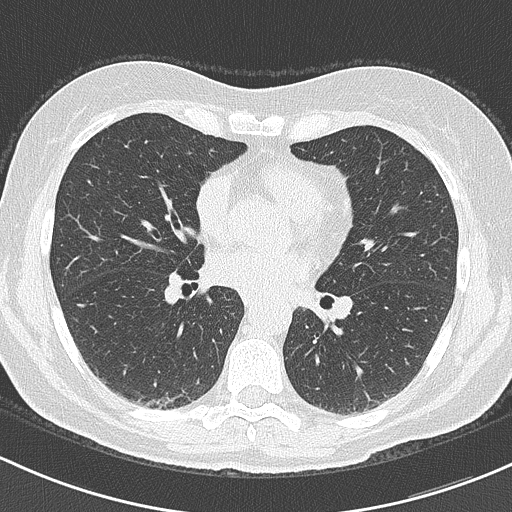
Low-dose screening chest CT, one axial slice. Position 101 of 201 along the scan axis. Reconstruction kernel B70f. 120 kVp. Lung window (W 1500 / L -600 HU). 512 × 512 image matrix, field of view 312 × 312 mm.
Structures marked on this image (expert manual segmentation):
- lesion 1 (tumor, upper lobe of right lung): box from (x=77, y=297) to (x=91, y=308) px